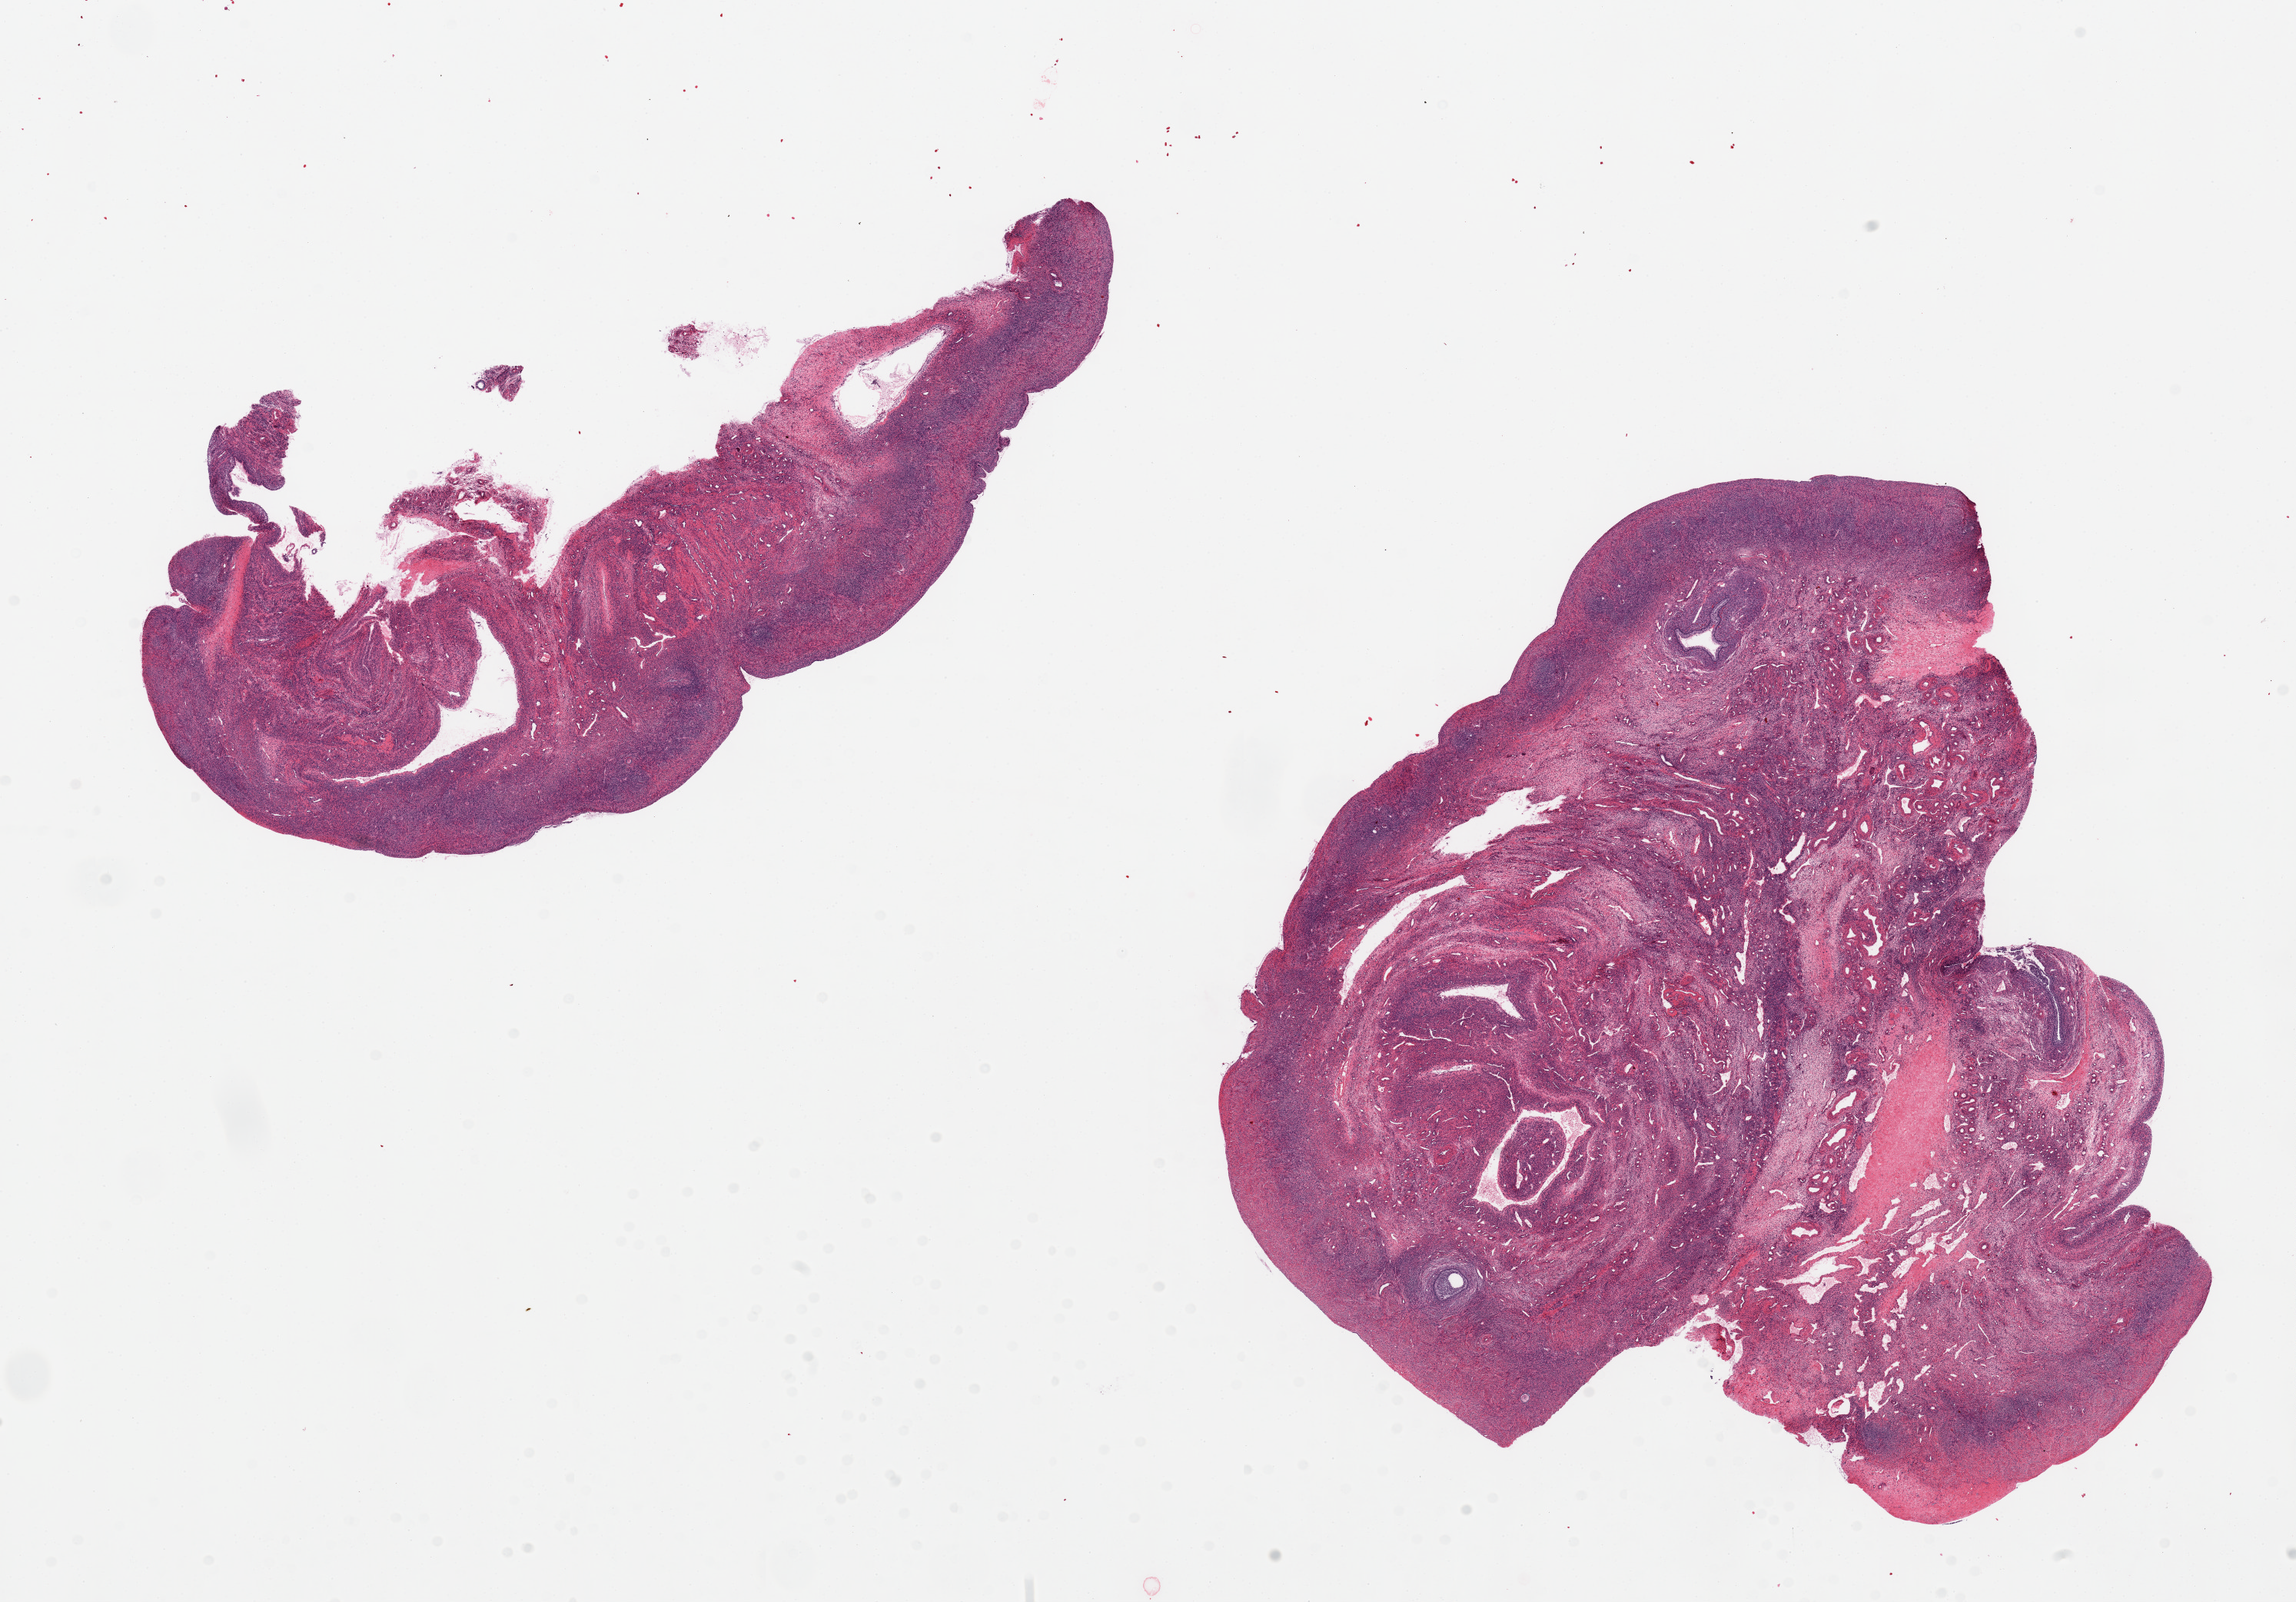
Digitized hematoxylin and eosin (H&E)-stained section — whole scanned area (about 23.6 x 16.5 mm, slide scanned at 20x) shown as a low-resolution overview. PAXgene-fixed, paraffin-embedded tissue. Sampled site (target tissue): ovary. Donor tissue sample. Female donor.
Pathologist's review note for this sample: 2 pieces.